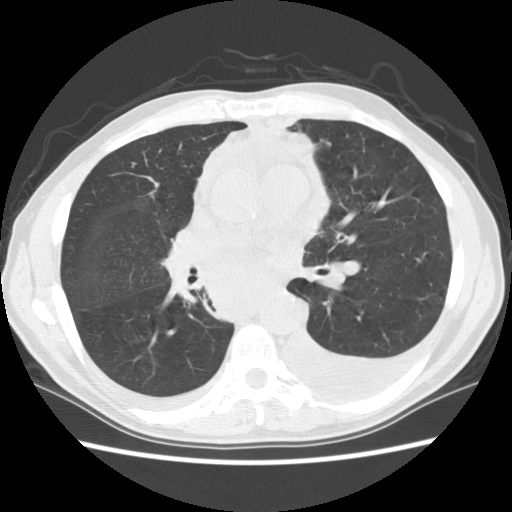
Axial slice from a low-dose chest CT screening exam. Baseline screening round. Lung window (W 1500 / L -600 HU). 2.5 mm slice thickness. Standard (soft-tissue) reconstruction kernel (STANDARD). 140 kVp. Slice 57 of 135 in the series. 512 × 512 image matrix, field of view 346 × 346 mm. Male participant, aged 60 years at enrolment. Current smoker at enrolment.
Lesion marked by an expert reader, bounding box [x1, y1, x2, y2] px = [175, 240, 303, 332]. No non-calcified nodule or mass ≥4 mm was recorded by the screening reader at this exam. Official screen result: negative screen, significant abnormalities not suspicious for lung cancer. Later outcome: lung cancer diagnosed 12 days after this screen — squamous cell carcinoma, NOS, carina, poorly differentiated (G3), stage IV (AJCC 6th edition).